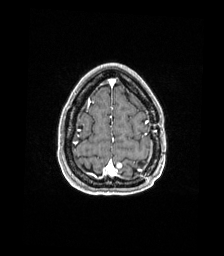
Brain MRI from a brain-tumour surgery series, one axial slice; position 38 of 176 along the scan axis; T1-weighted post-contrast; 224 × 256 image matrix, field of view 224 × 256 mm. Case-level facts recorded for this patient, not image findings: histopathology: Atypical meningioma; WHO grade: 2; tumour location: Paramedian Left Parietal.
Structures marked on this image (outlined manually by an expert reader):
- previous resection cavity: bounding box [x1, y1, x2, y2] px = [139, 161, 143, 166]
- tumour: [116, 162, 122, 169]